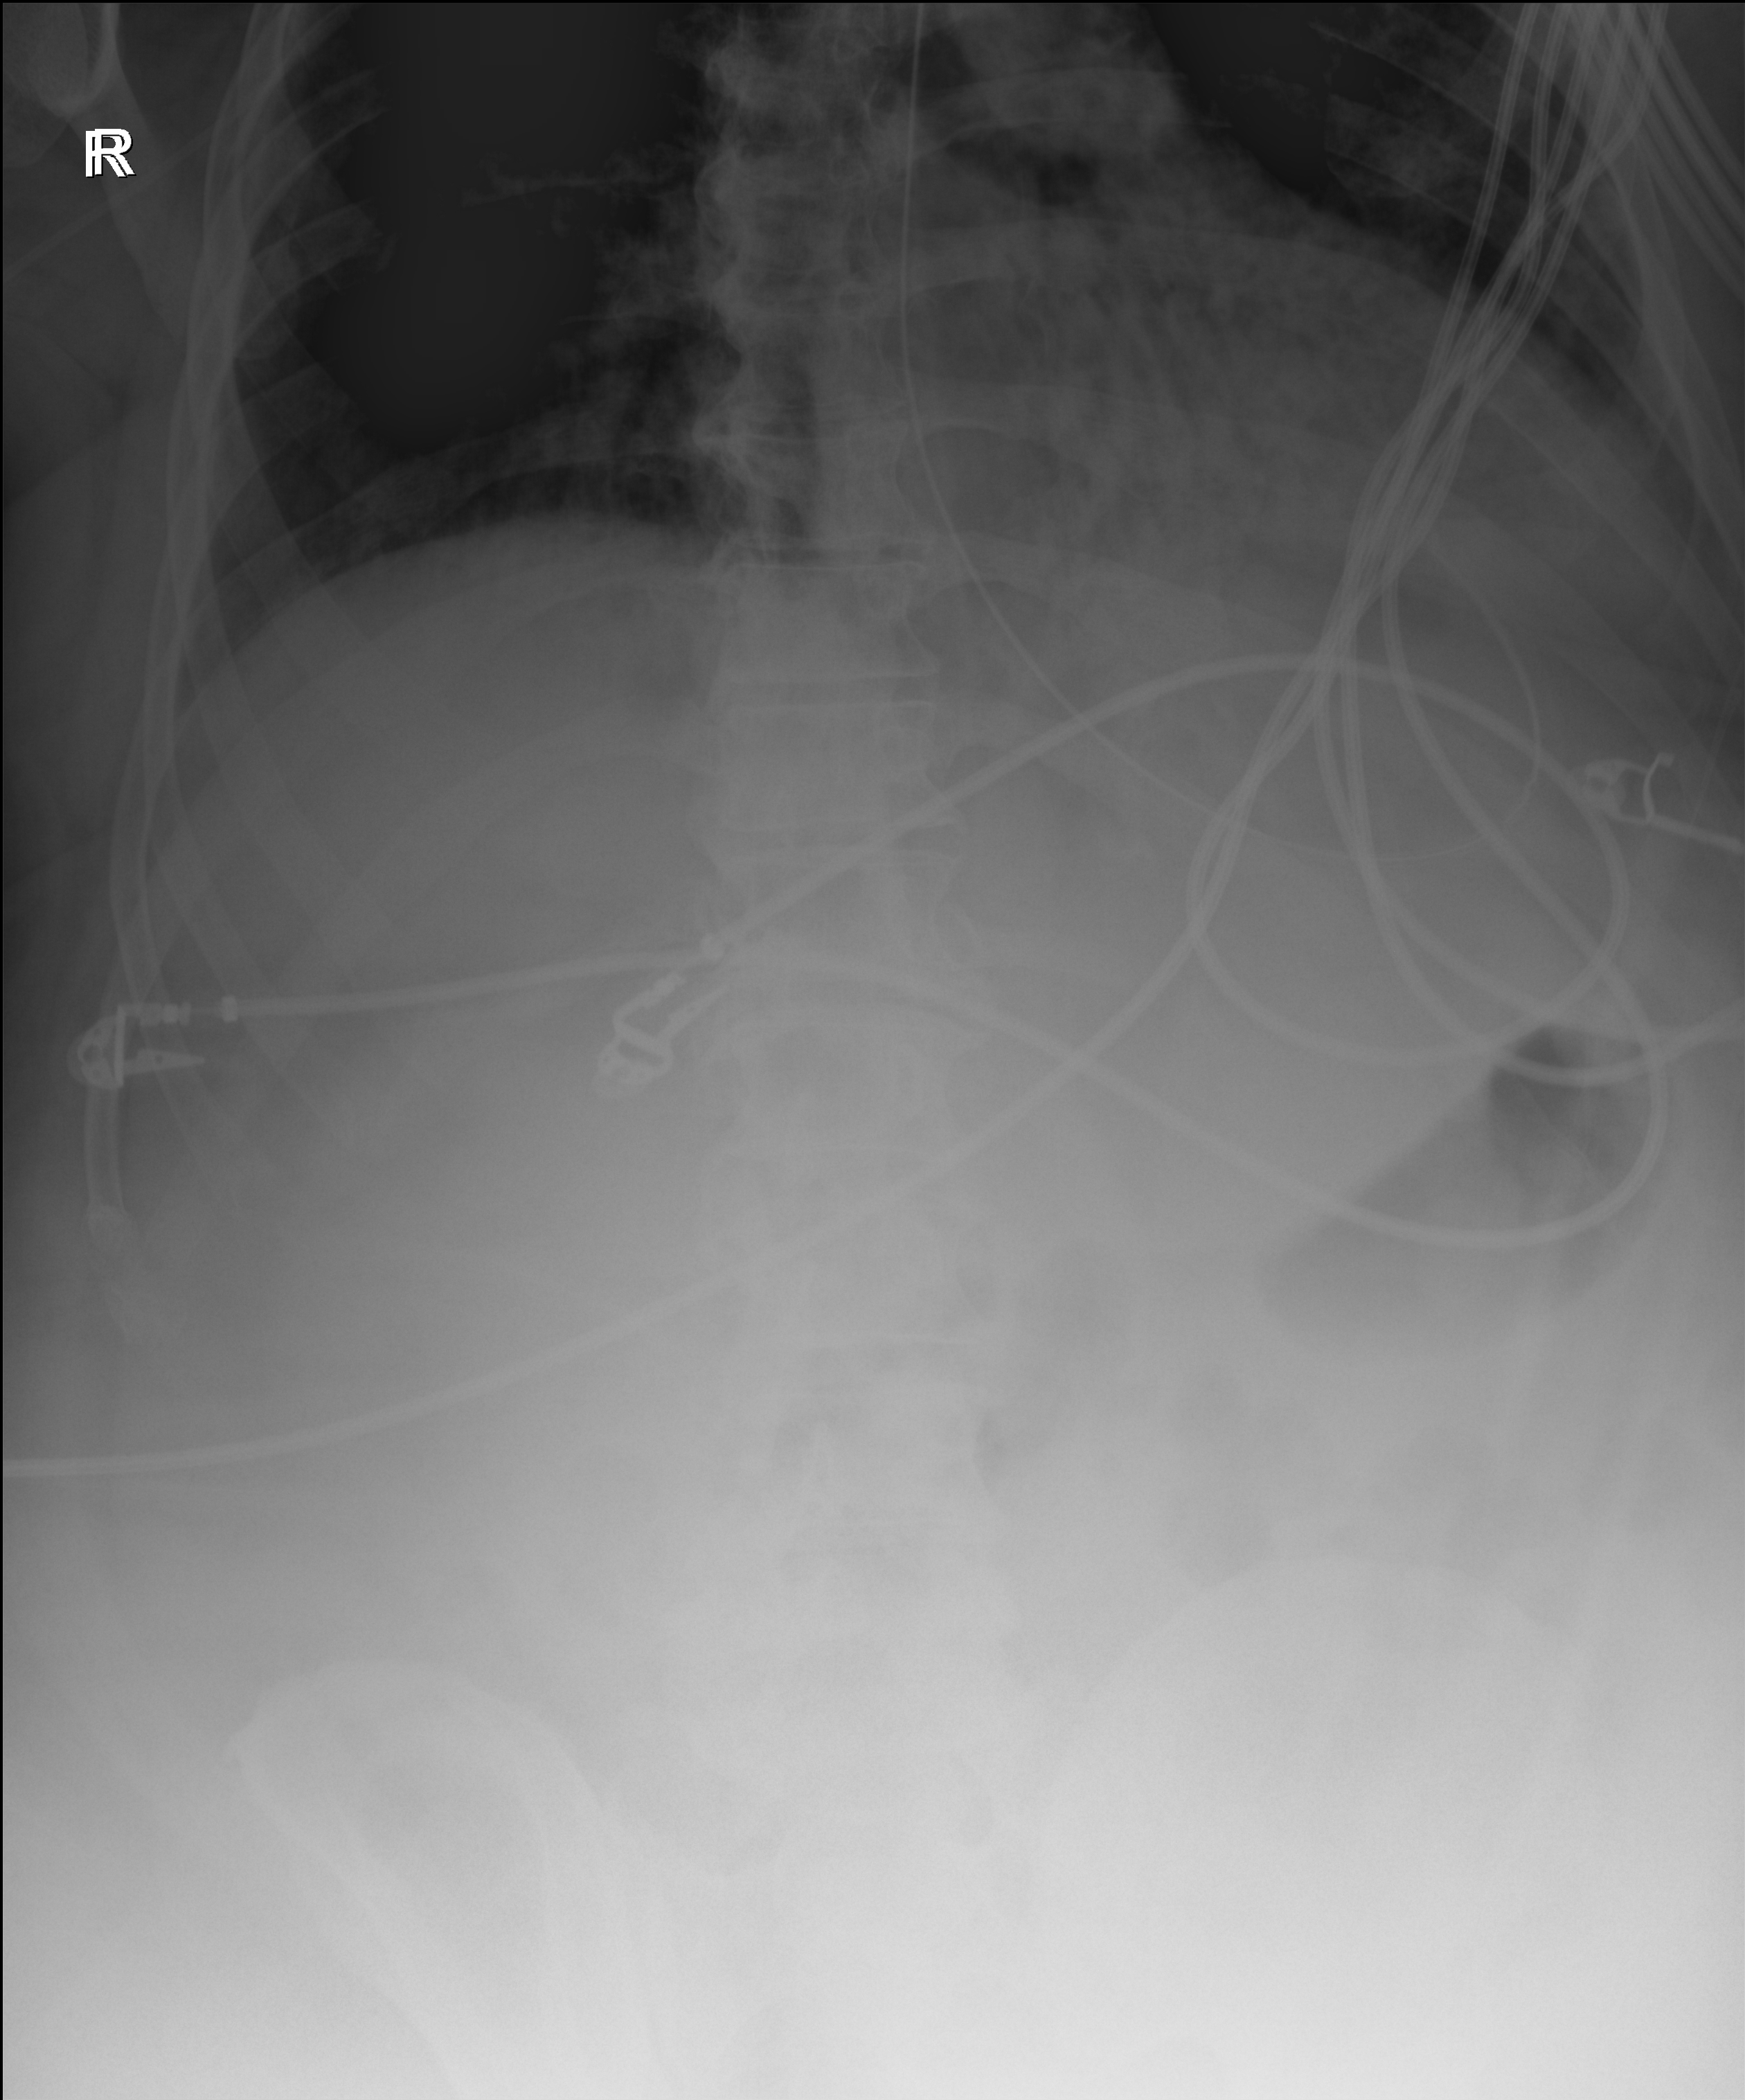
Portable abdomen radiograph; anteroposterior (AP) projection. Patient hospitalised with COVID-19, aged 18–59 years.
Admission-level facts for this patient (not findings on this image; timing relative to this image not recorded): mechanically ventilated during this hospital stay: yes.